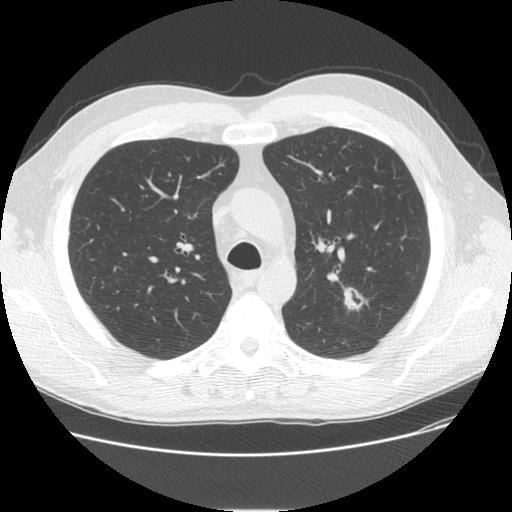
Low-dose screening chest CT, one axial slice; slice 111 of 150 in the series (ordered by position); reconstruction kernel STANDARD; 120 kVp; lung window (W 1500 / L -600 HU); 512 × 512 image matrix.
Outlined on this slice (manually delineated by an expert):
- lesion 1 (tumor, upper lobe of left lung): bounding box <344,288,363,310> (left, top, right, bottom; pixels)